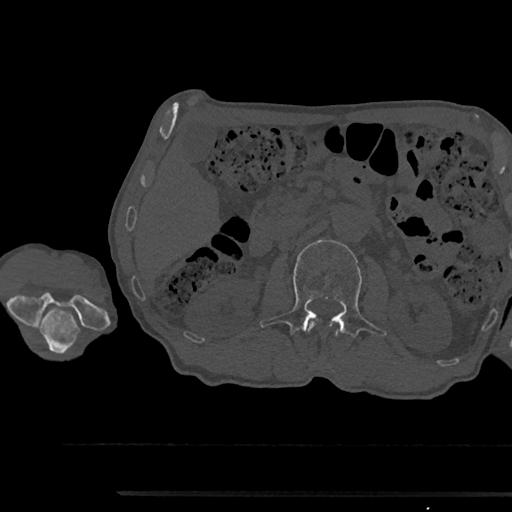
CT including the spine, one axial slice. Position 577 of 797 along the scan axis. Reconstruction kernel Br40s/3. 120 kVp. Bone window (W 1800 / L 400 HU). 0.5 mm slice thickness. 512 × 512 image matrix. Male patient, age 79 years. Case-level facts recorded for this patient, not image findings: primary cancer: prostate.
Outlined on this slice (semi-automatically segmented with operator editing):
- L1 vertebra: bounding box [x1, y1, x2, y2] px = [308, 322, 313, 331]
- L2 vertebra: [260, 240, 386, 362]